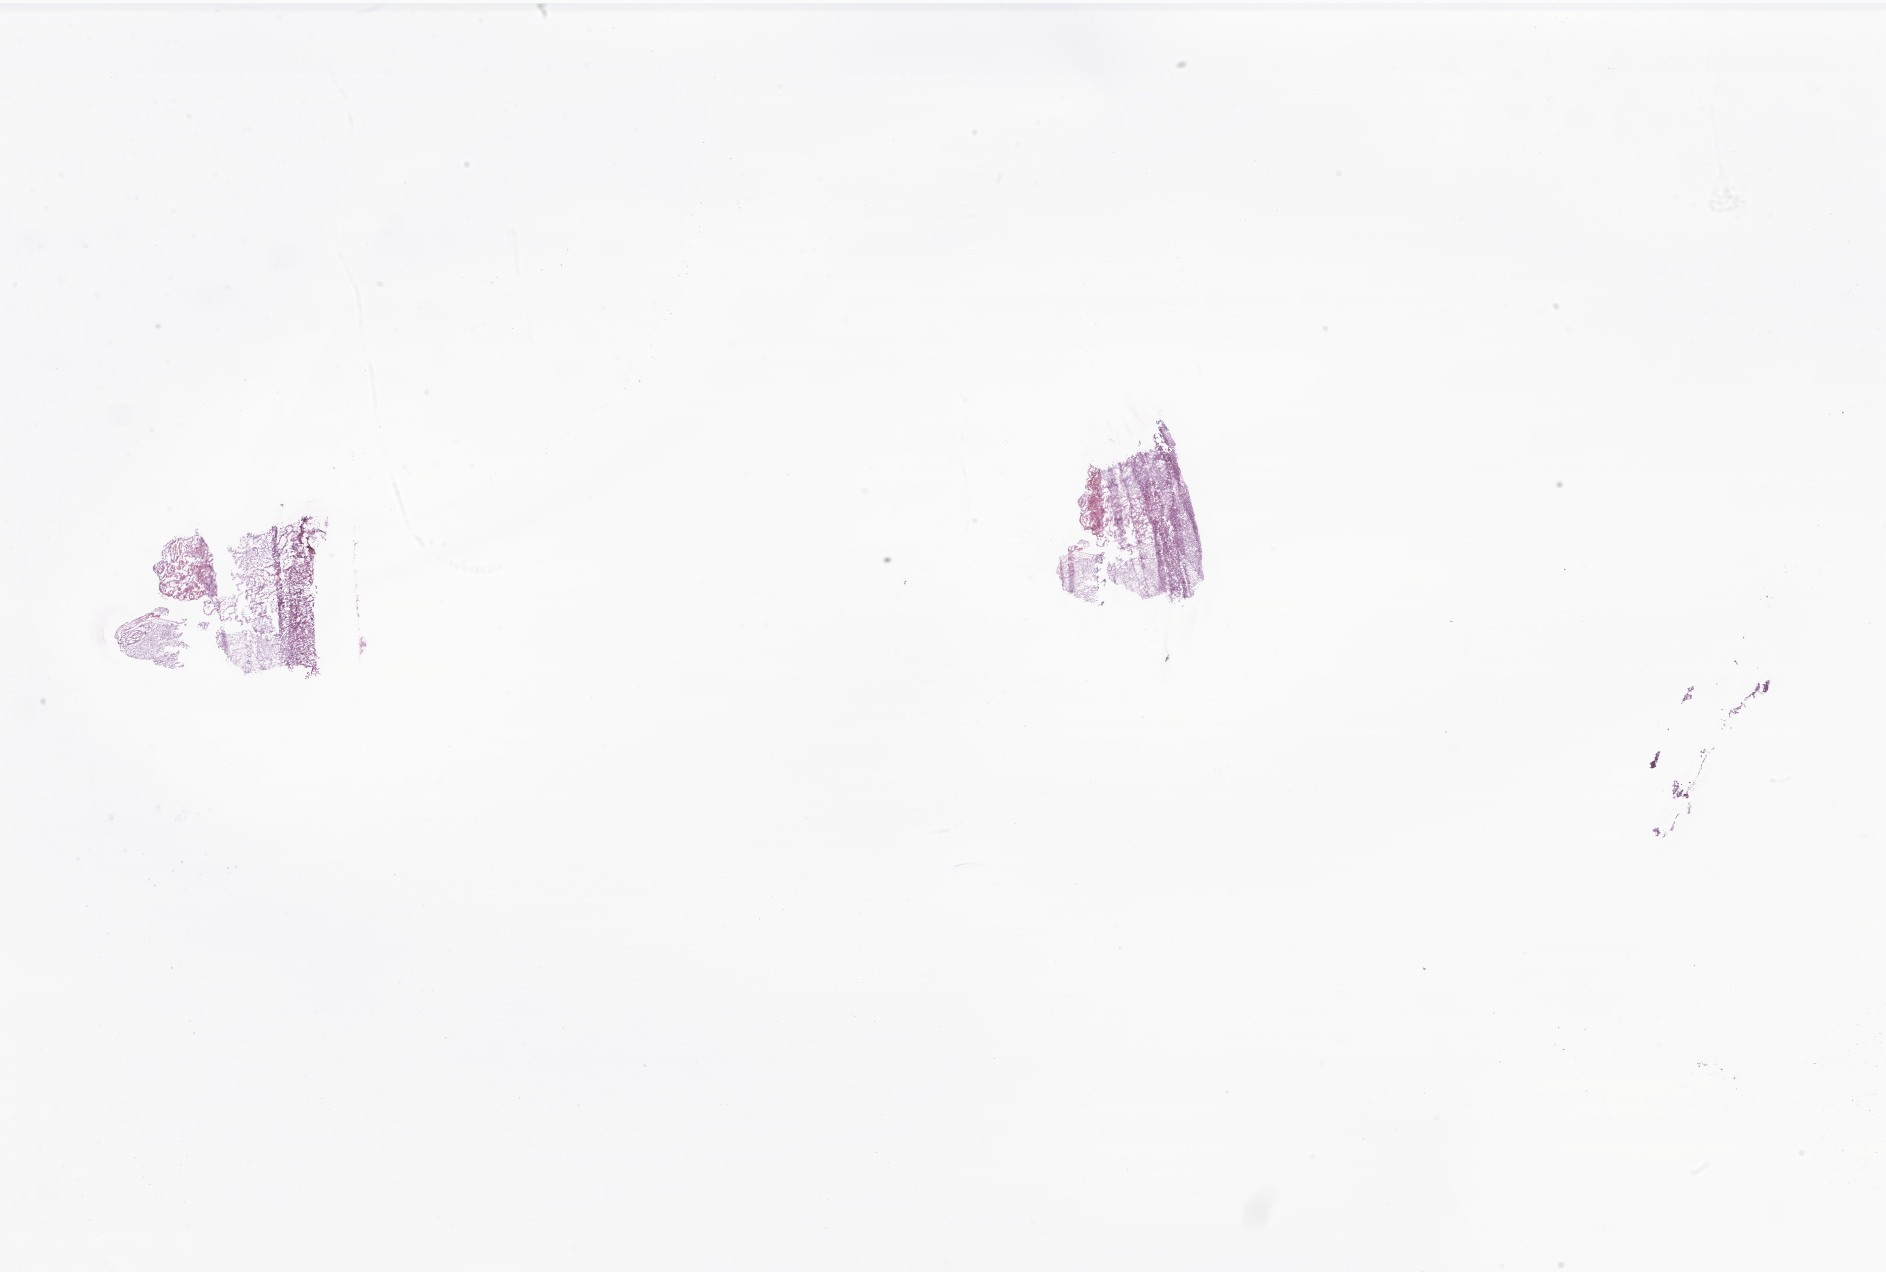
Haematoxylin and eosin whole-slide image of tumor tissue from the brain — shown as a low-resolution overview of the whole scanned area (about 31.8 x 21.5 mm). Cryosection (OCT / tissue freezing medium). Patient: female, age 155 days.
* diagnosis: Glioma, malignant